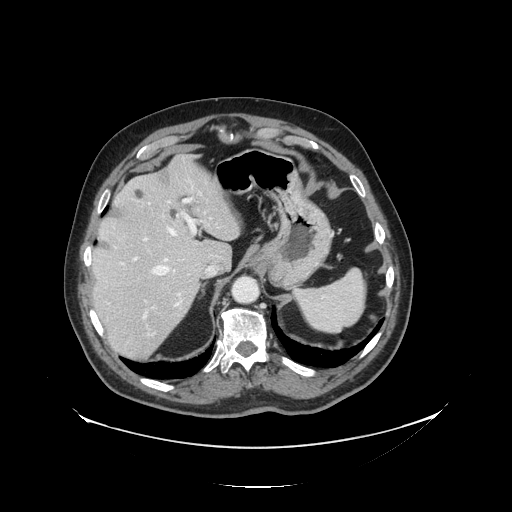
Contrast-enhanced abdominal CT, one axial slice. Position 101 of 138 along the scan axis. Reconstruction kernel STANDARD. 120 kVp. Soft-tissue window (W 400 / L 40 HU). 2.5 mm slice thickness. 512 × 512 image matrix, field of view 497 × 497 mm. Male patient, age 77 years. Case-level facts recorded for this patient, not image findings: diagnosis: colorectal cancer liver metastases, imaged before liver resection; multiple liver metastases: no; largest metastasis: 1.5 cm.
Outlined on this slice (outlined manually by an expert reader):
- hepatic veins: bounding box <151,217,212,307> (left, top, right, bottom; pixels)
- liver: <92,157,240,360>
- planned liver remnant (the part of the liver to remain after resection): <92,158,240,288>
- portal vein (with intrahepatic branches): <133,197,220,319>
- liver metastasis: <169,209,180,220>
- liver metastasis: <135,189,145,199>